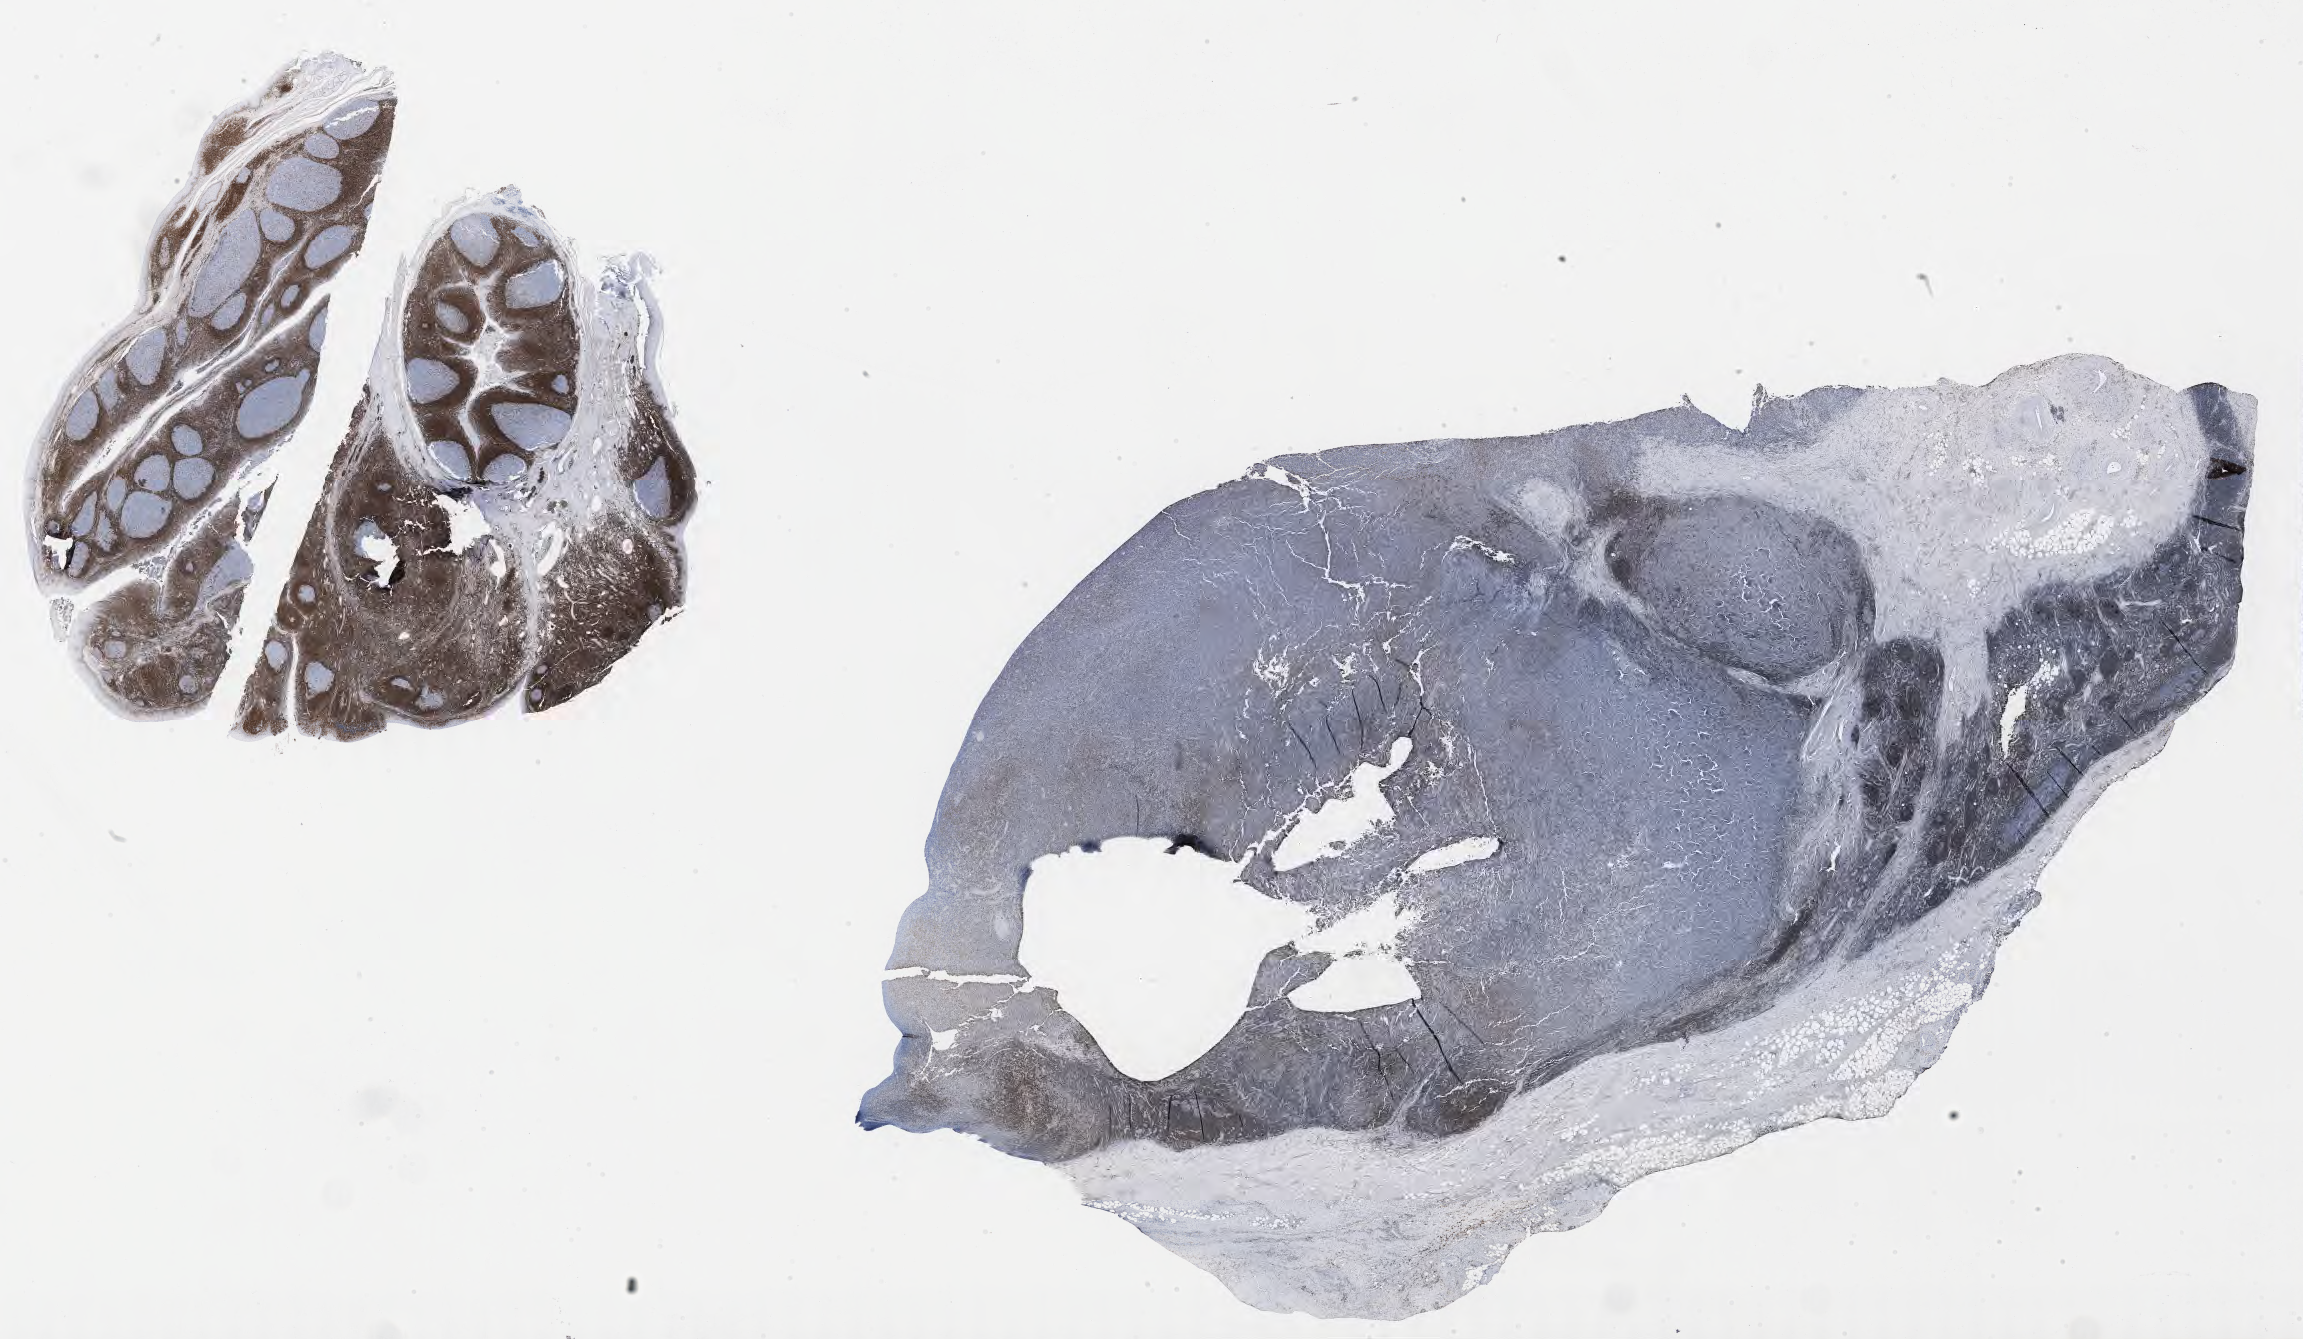
Whole-slide image, immunohistochemical stain for BCL2, whole scanned area (about 37.2 x 21.6 mm) shown as a low-resolution overview. Specimen: tumor tissue. Site: lymph node. Patient: male, 60 years old.
Histologic diagnosis: Diffuse large B-cell lymphoma, NOS.